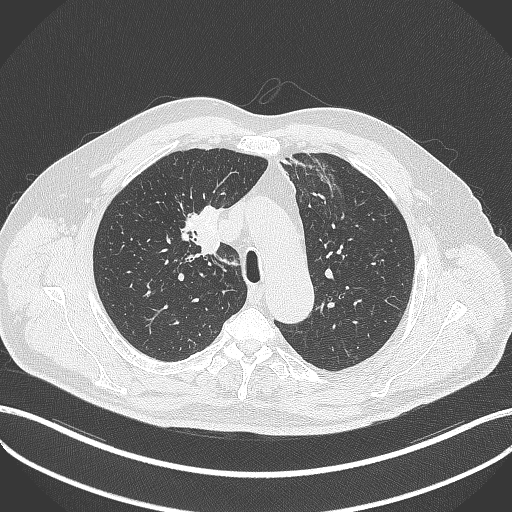
Chest CT, one axial slice. Position 287 of 411 along the scan axis. Reconstruction kernel B70f. Lung window (W 1500 / L -600 HU). 1 mm slice thickness. 512 × 512 image matrix. Patient: male, 60 years. From the clinical record (not read from this slice): clinical TNM (as recorded): T1b N1 M0.
Structures marked on this image (bounding box drawn by a radiologist):
- lung tumour (recorded histology: squamous cell carcinoma): bounding box <182,196,223,259> (left, top, right, bottom; pixels)